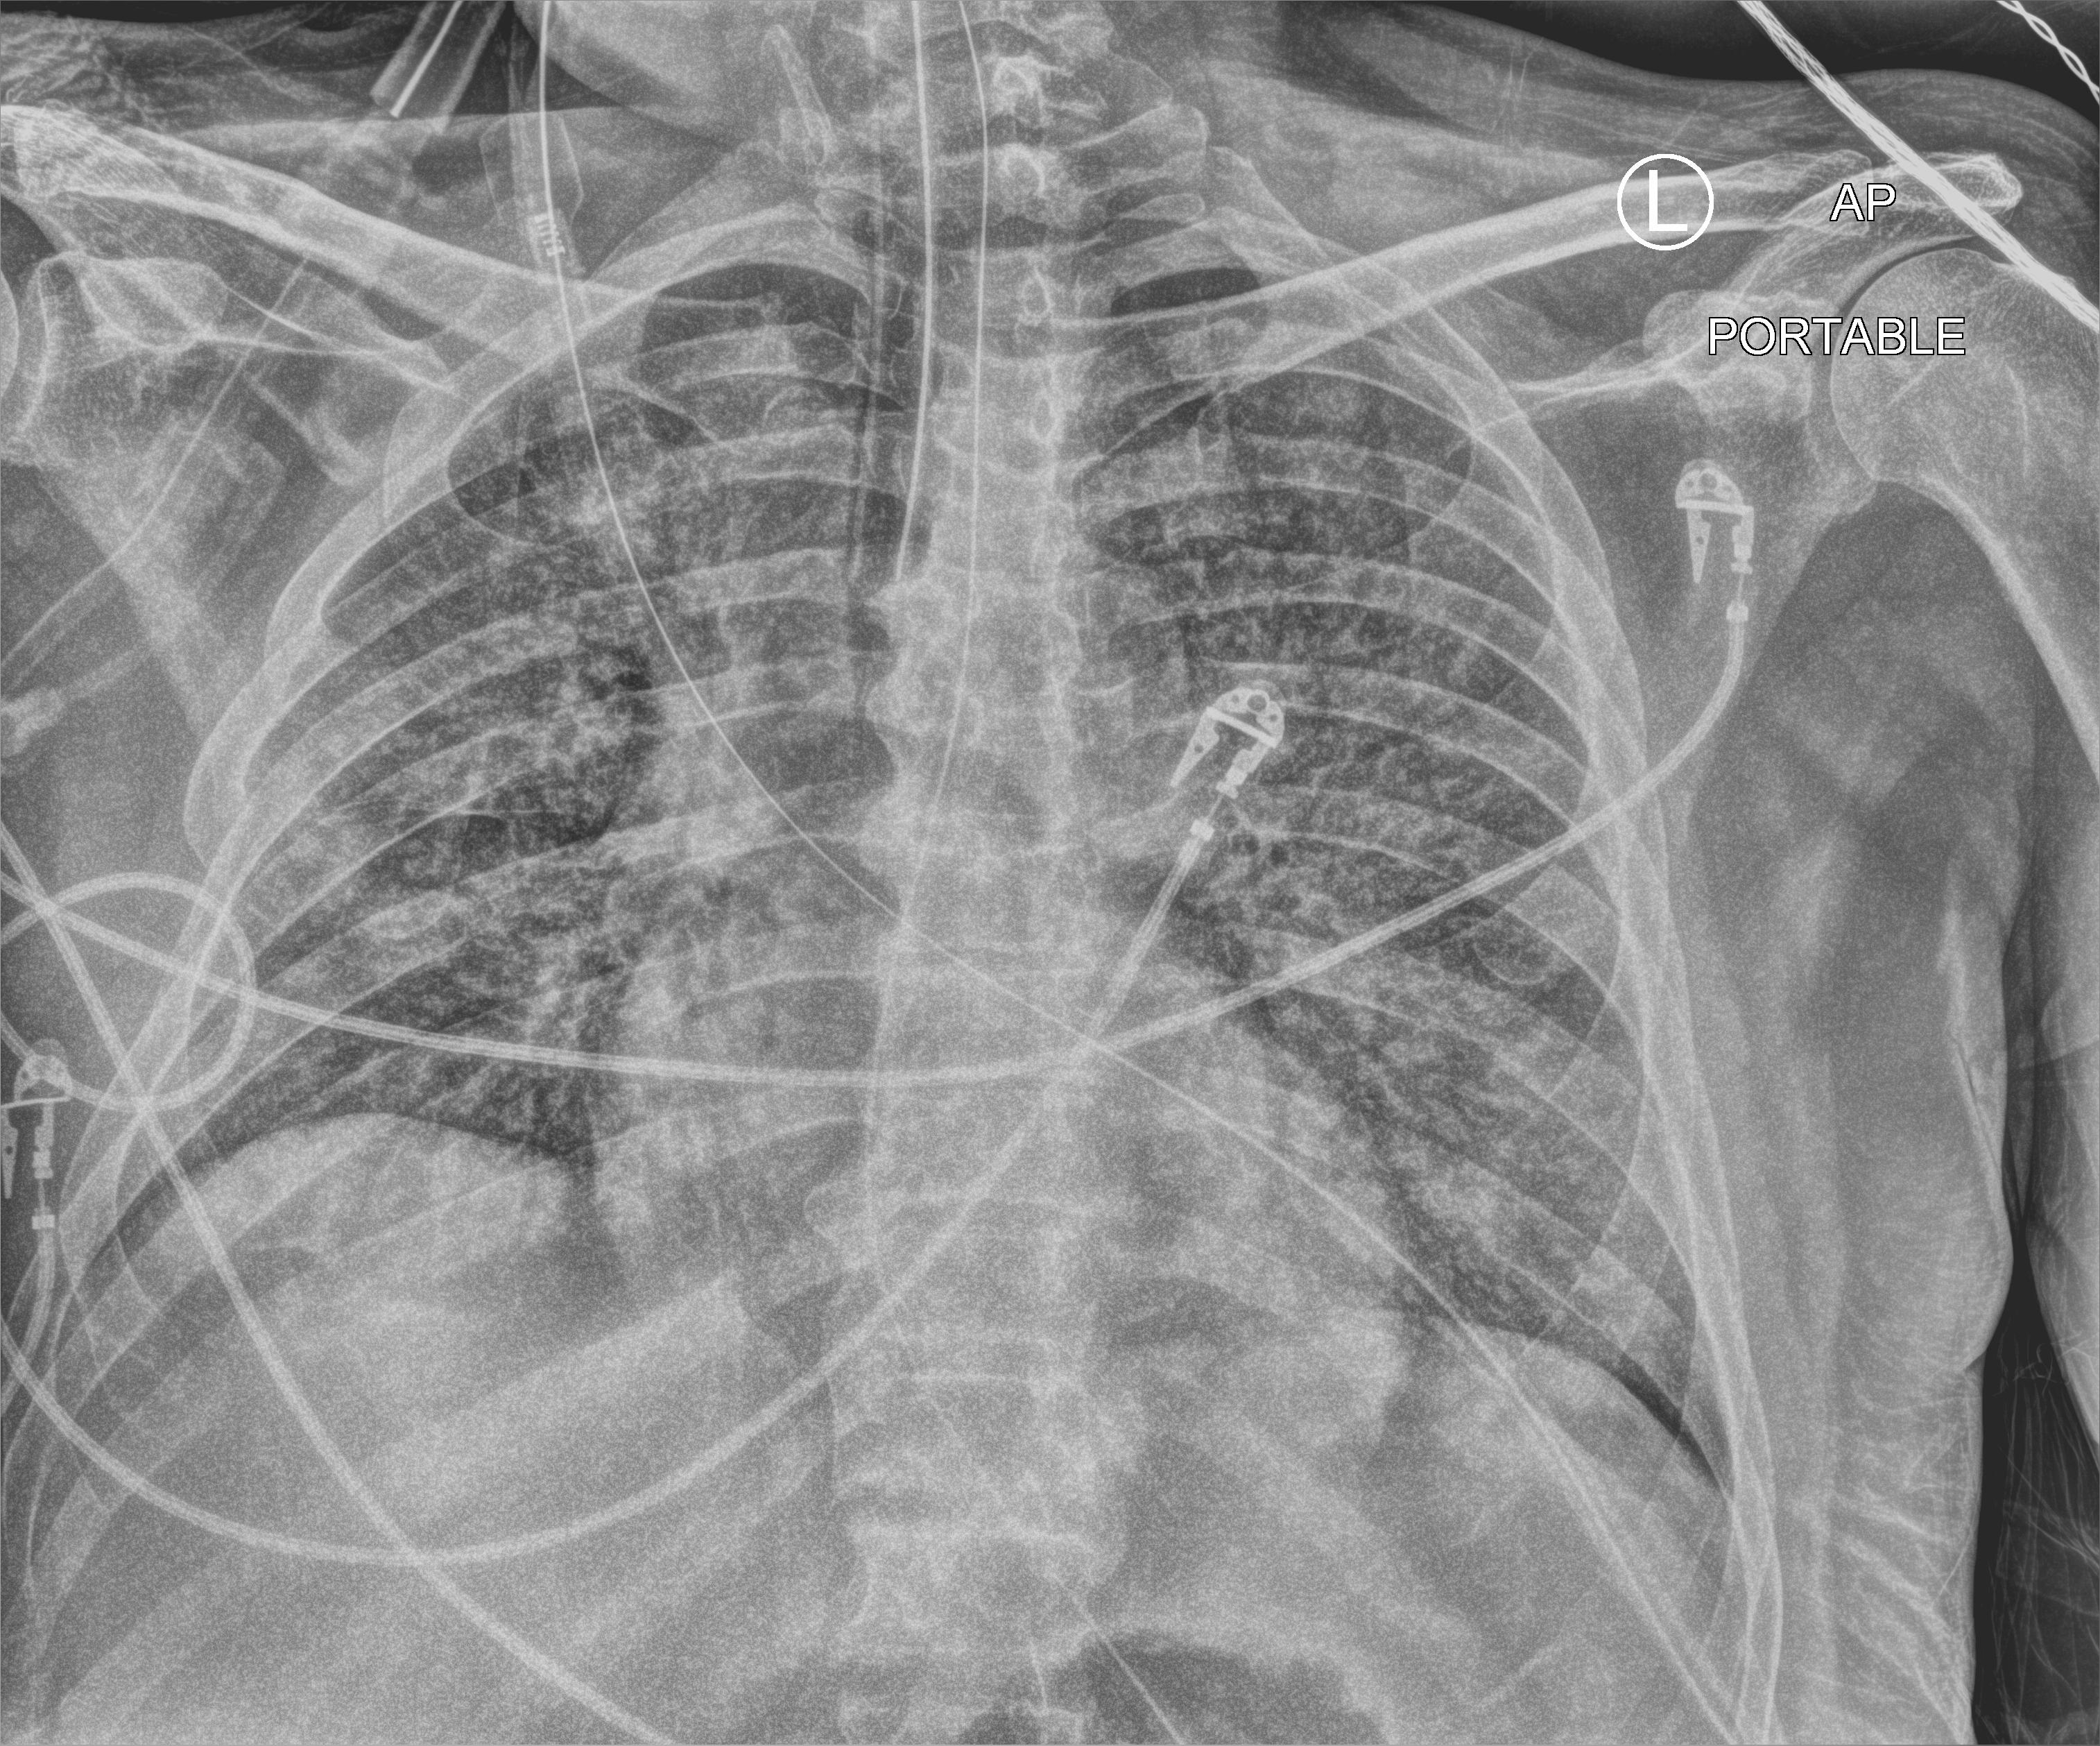
Chest X-ray (portable); anteroposterior (AP) projection. Male patient hospitalised with COVID-19, age 60–74 years.
Admission-level facts for this patient (not findings on this image; timing relative to this image not recorded):
- COPD (admission record): no